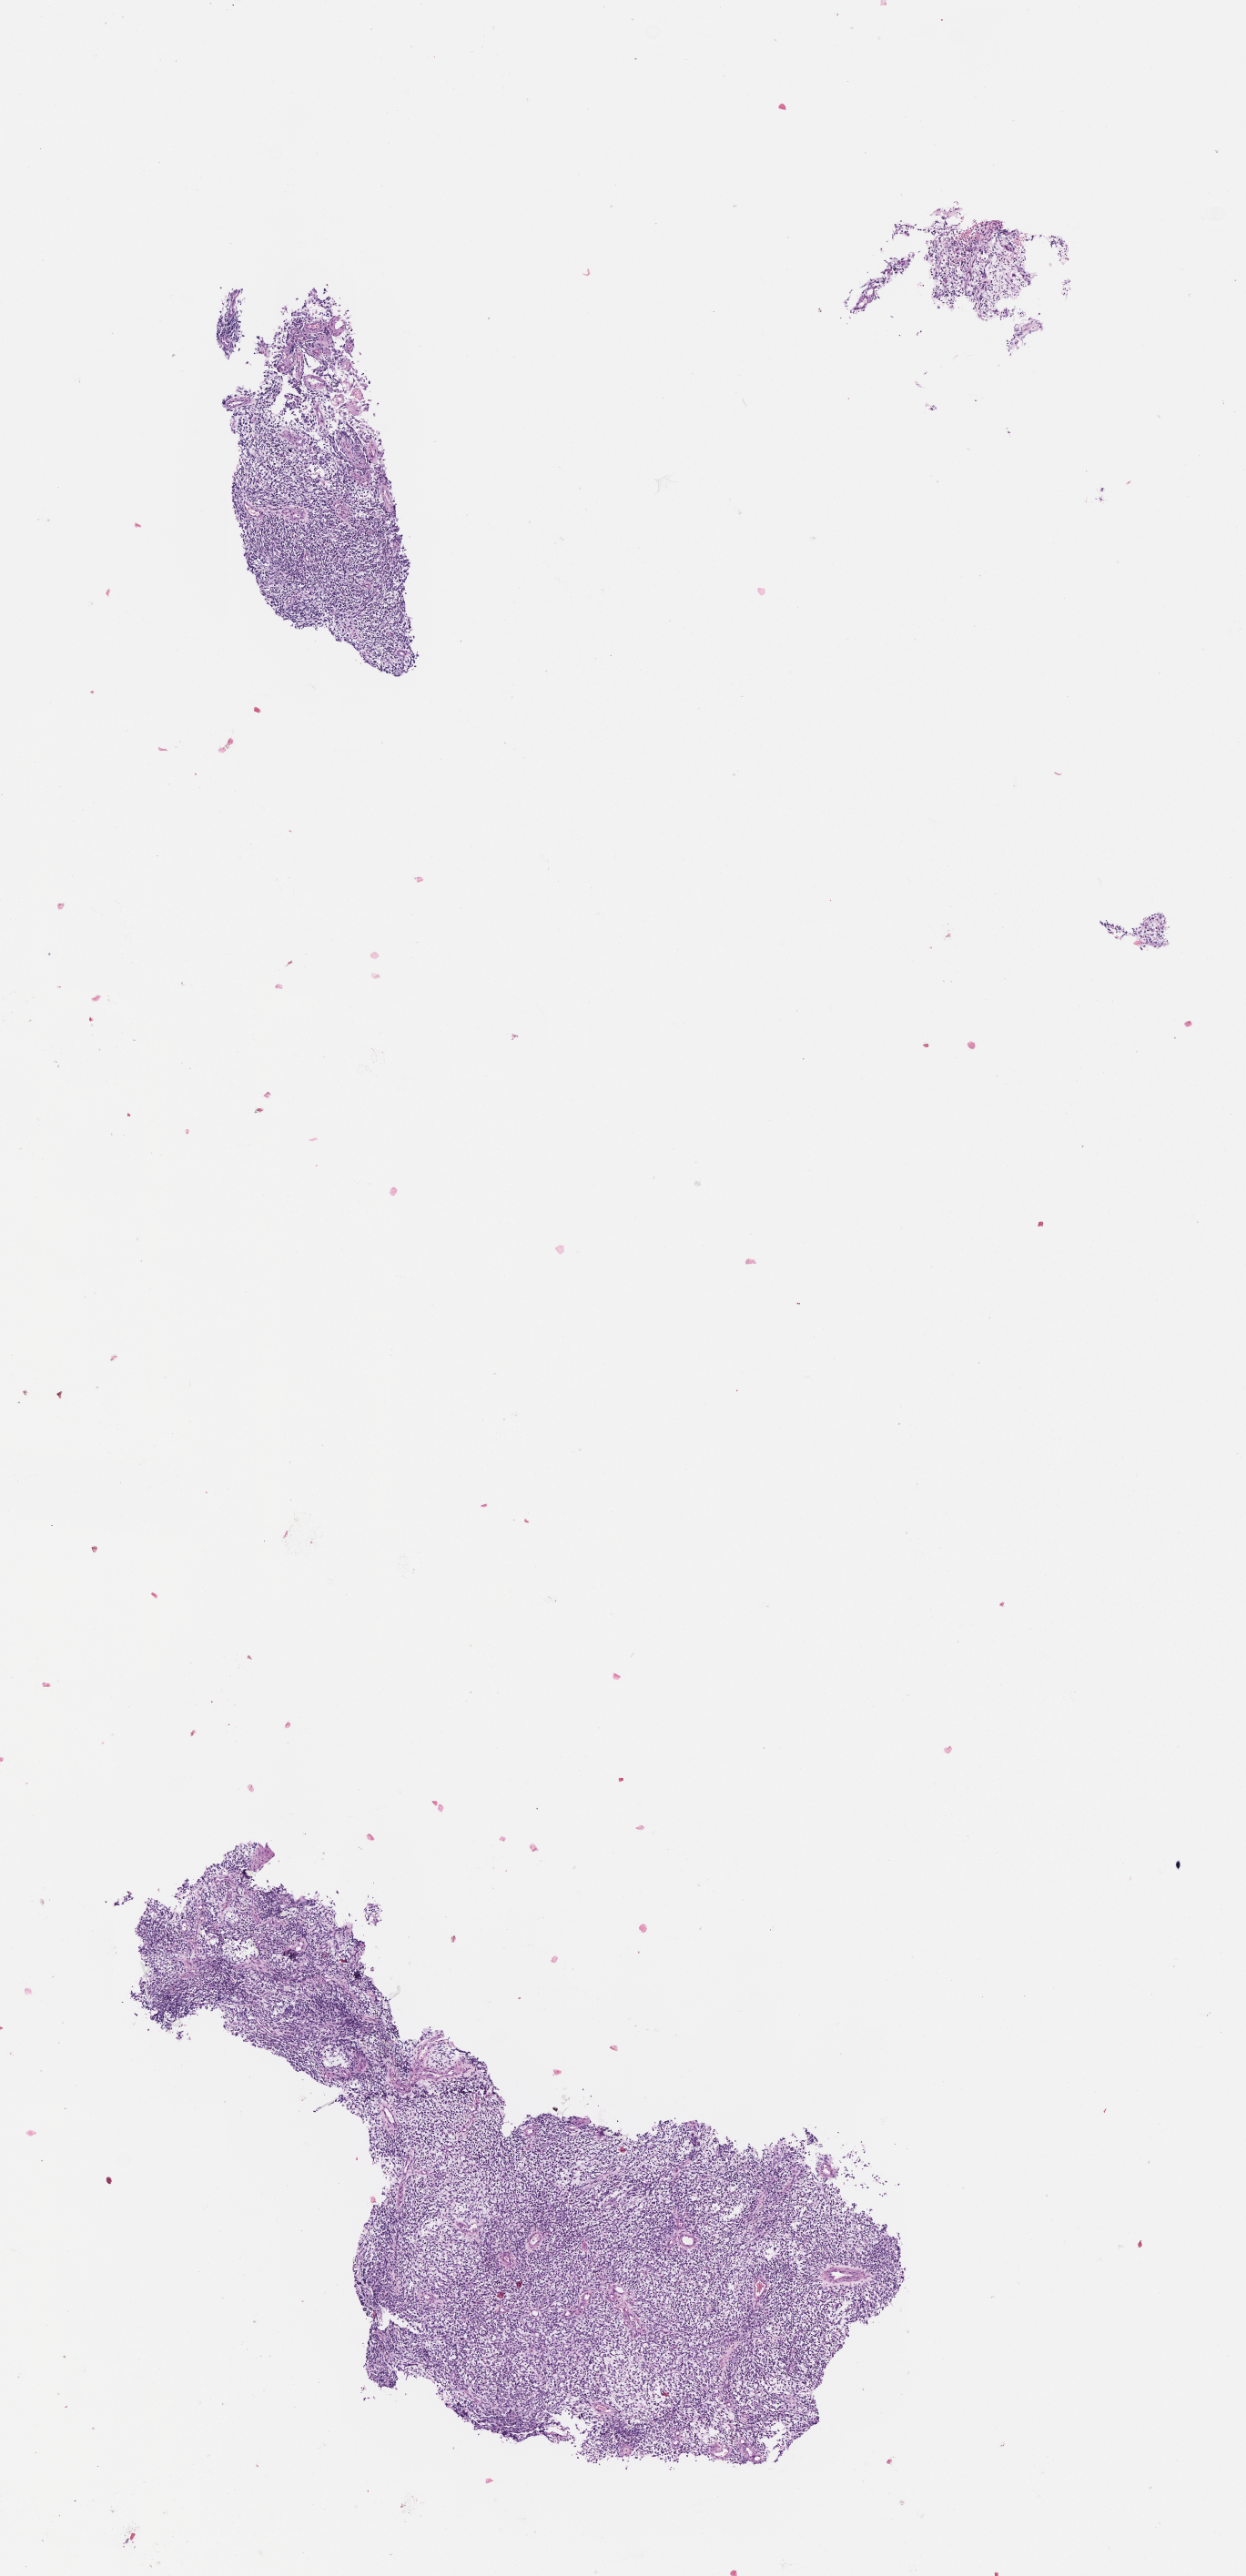
Digitized haematoxylin and eosin-stained section of tumor tissue — a low-resolution overview of the entire scanned area, about 5.5 x 11.4 mm; formalin-fixed paraffin-embedded section; sample anatomic site: bladder. Patient: male, age 5.8 years at diagnosis.
Diagnosis: rhabdomyosarcoma; histological classification: embryonal rhabdomyosarcoma.